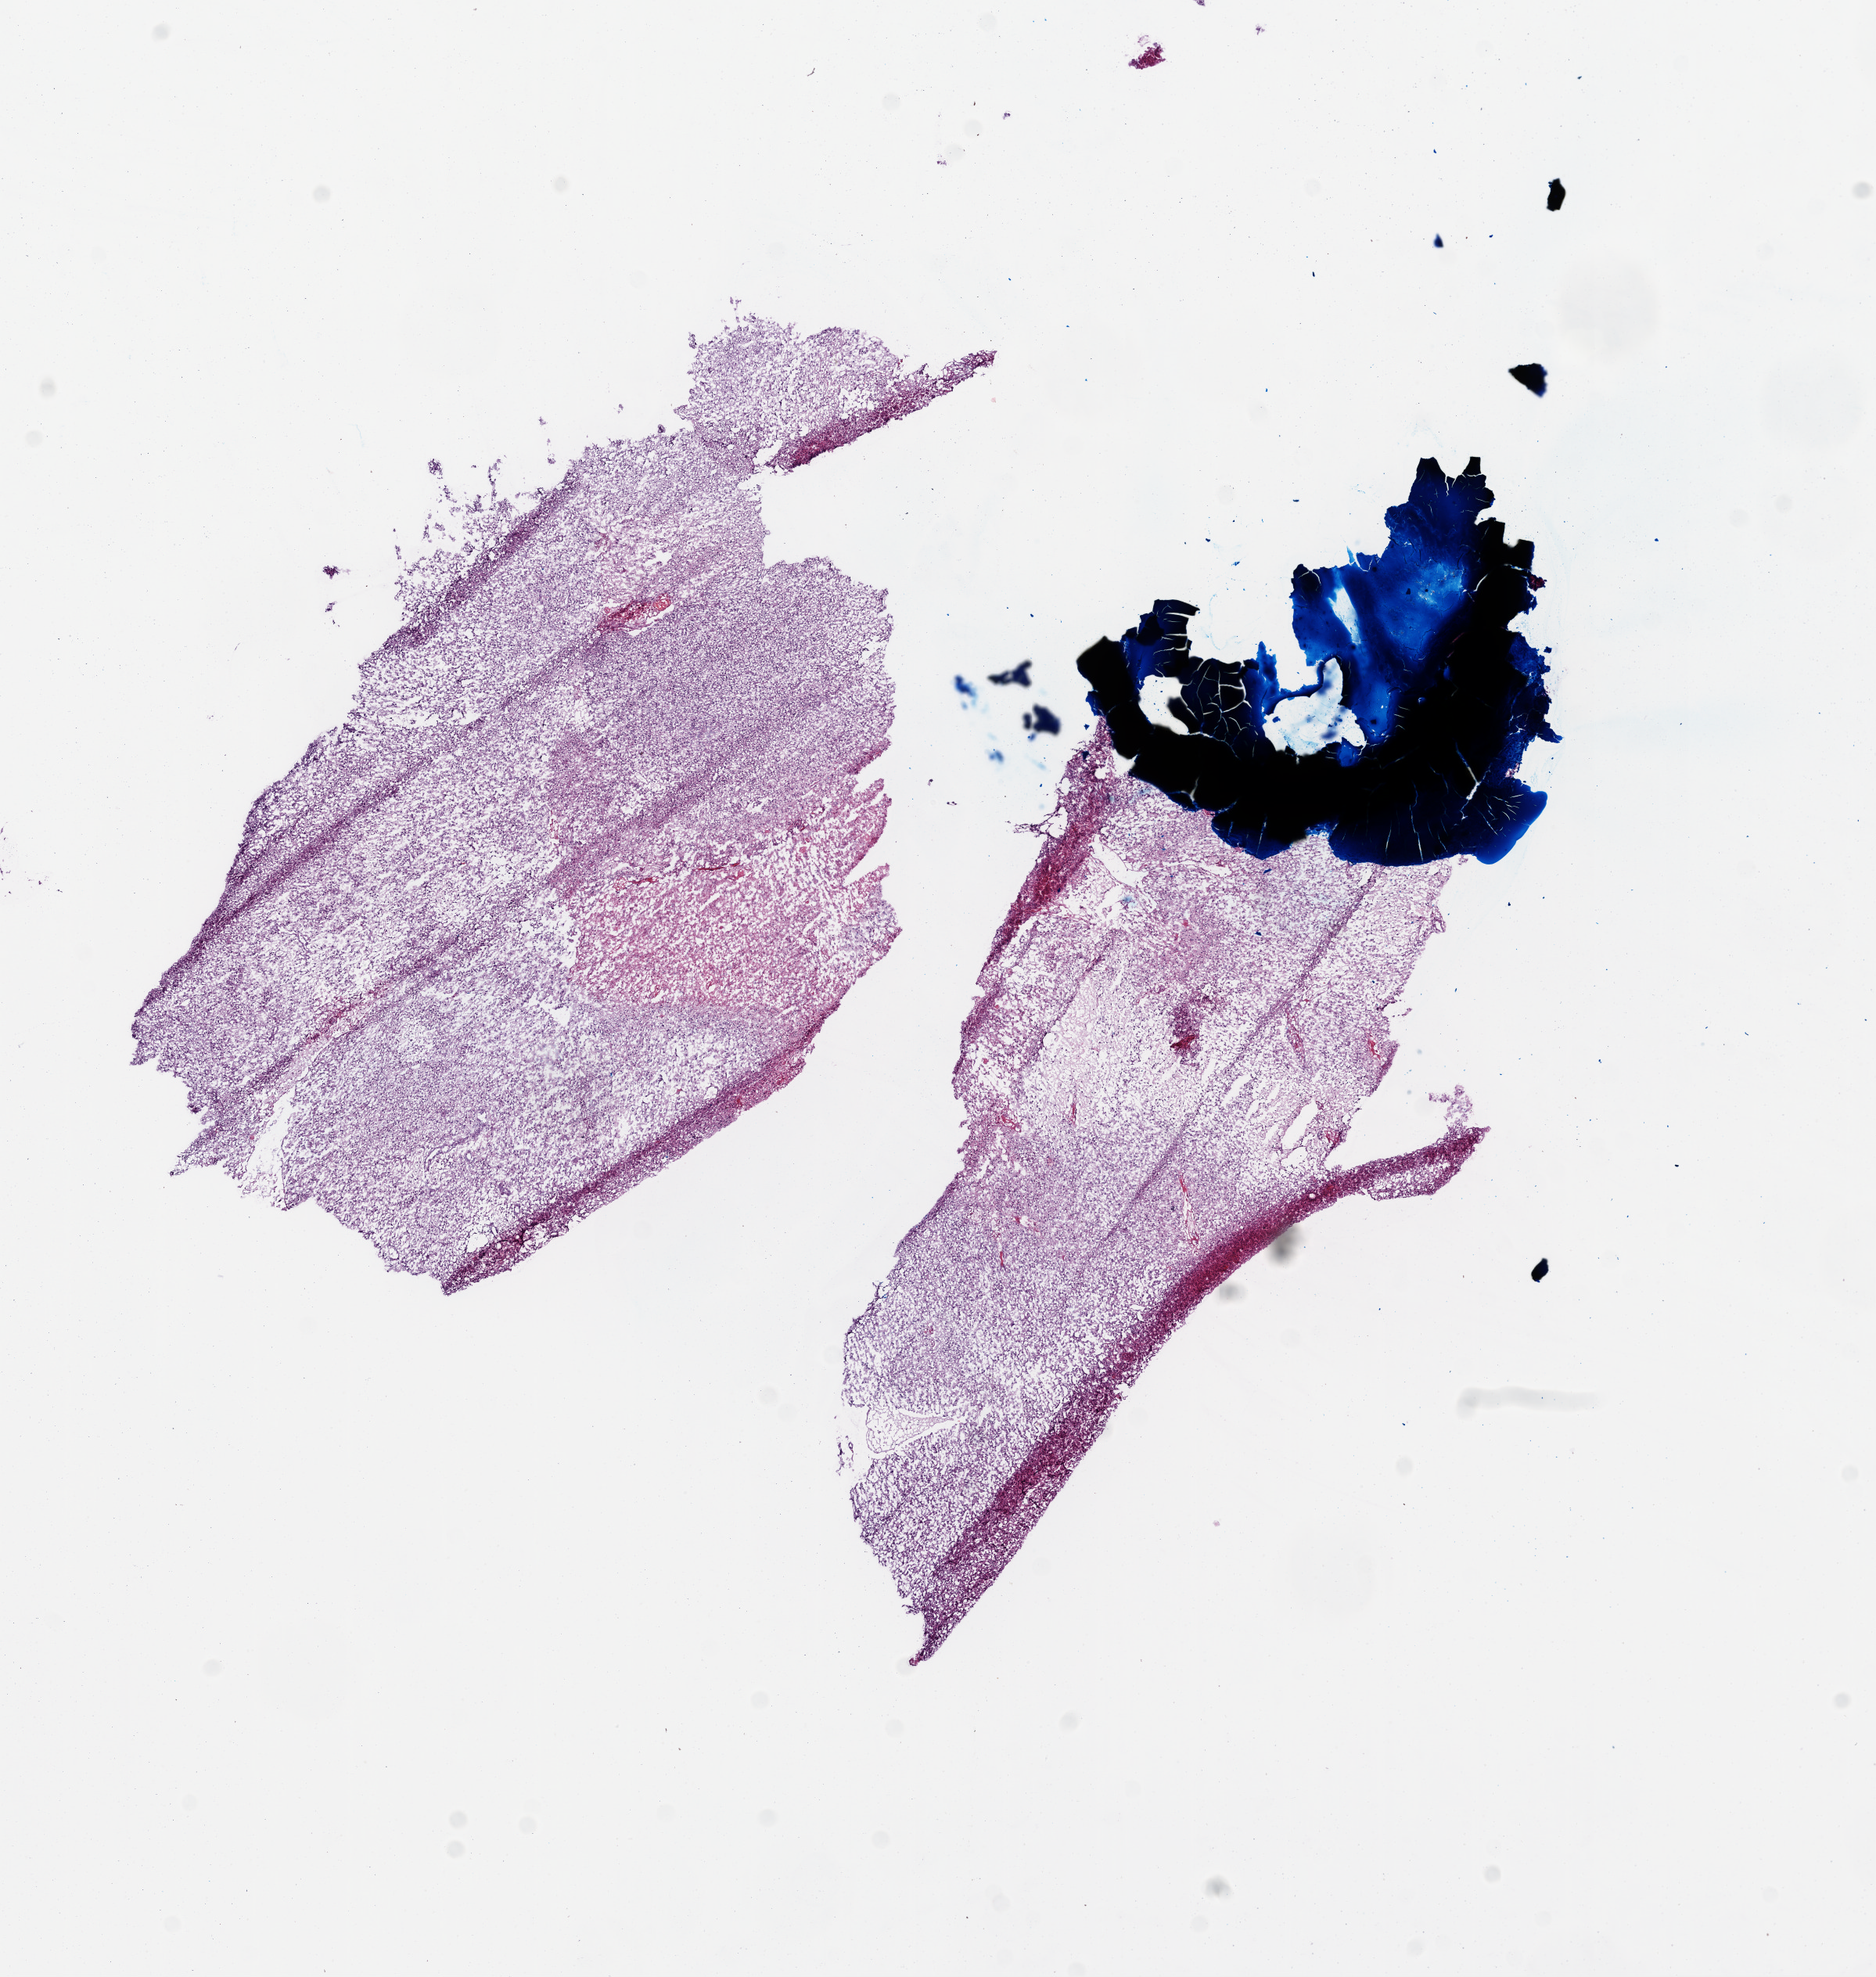
H&E-stained whole-slide image, whole scanned area (about 9.7 x 10.2 mm, slide scanned at 20x) shown as a low-resolution overview, frozen section from the top of the tissue portion, sample: primary tumour, brain. Female, age 56 years at initial diagnosis. Composition of this section per pathologist review: tumour cells 80%, tumour nuclei 85%, normal cells 0%, stromal cells 10%, necrosis 10%.
Histologic diagnosis: Glioblastoma.